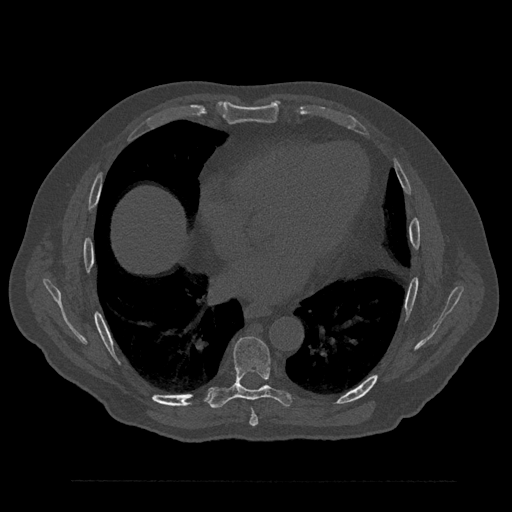
CT including the spine, one axial slice. Slice 460 of 797 in the series (ordered by position). Reconstruction kernel Br40s/3. 120 kVp. Bone window (W 1800 / L 400 HU). 0.5 mm slice thickness. 512 × 512 image matrix, field of view 430 × 430 mm. Patient: male, 61 years. From the clinical record (not read from this slice): primary cancer: prostate.
Outlined on this slice (semi-automatic segmentation, software-assisted and operator-edited):
- T7 vertebra: bounding box <250,409,258,426> (left, top, right, bottom; pixels)
- T8 vertebra: <208,336,293,409>